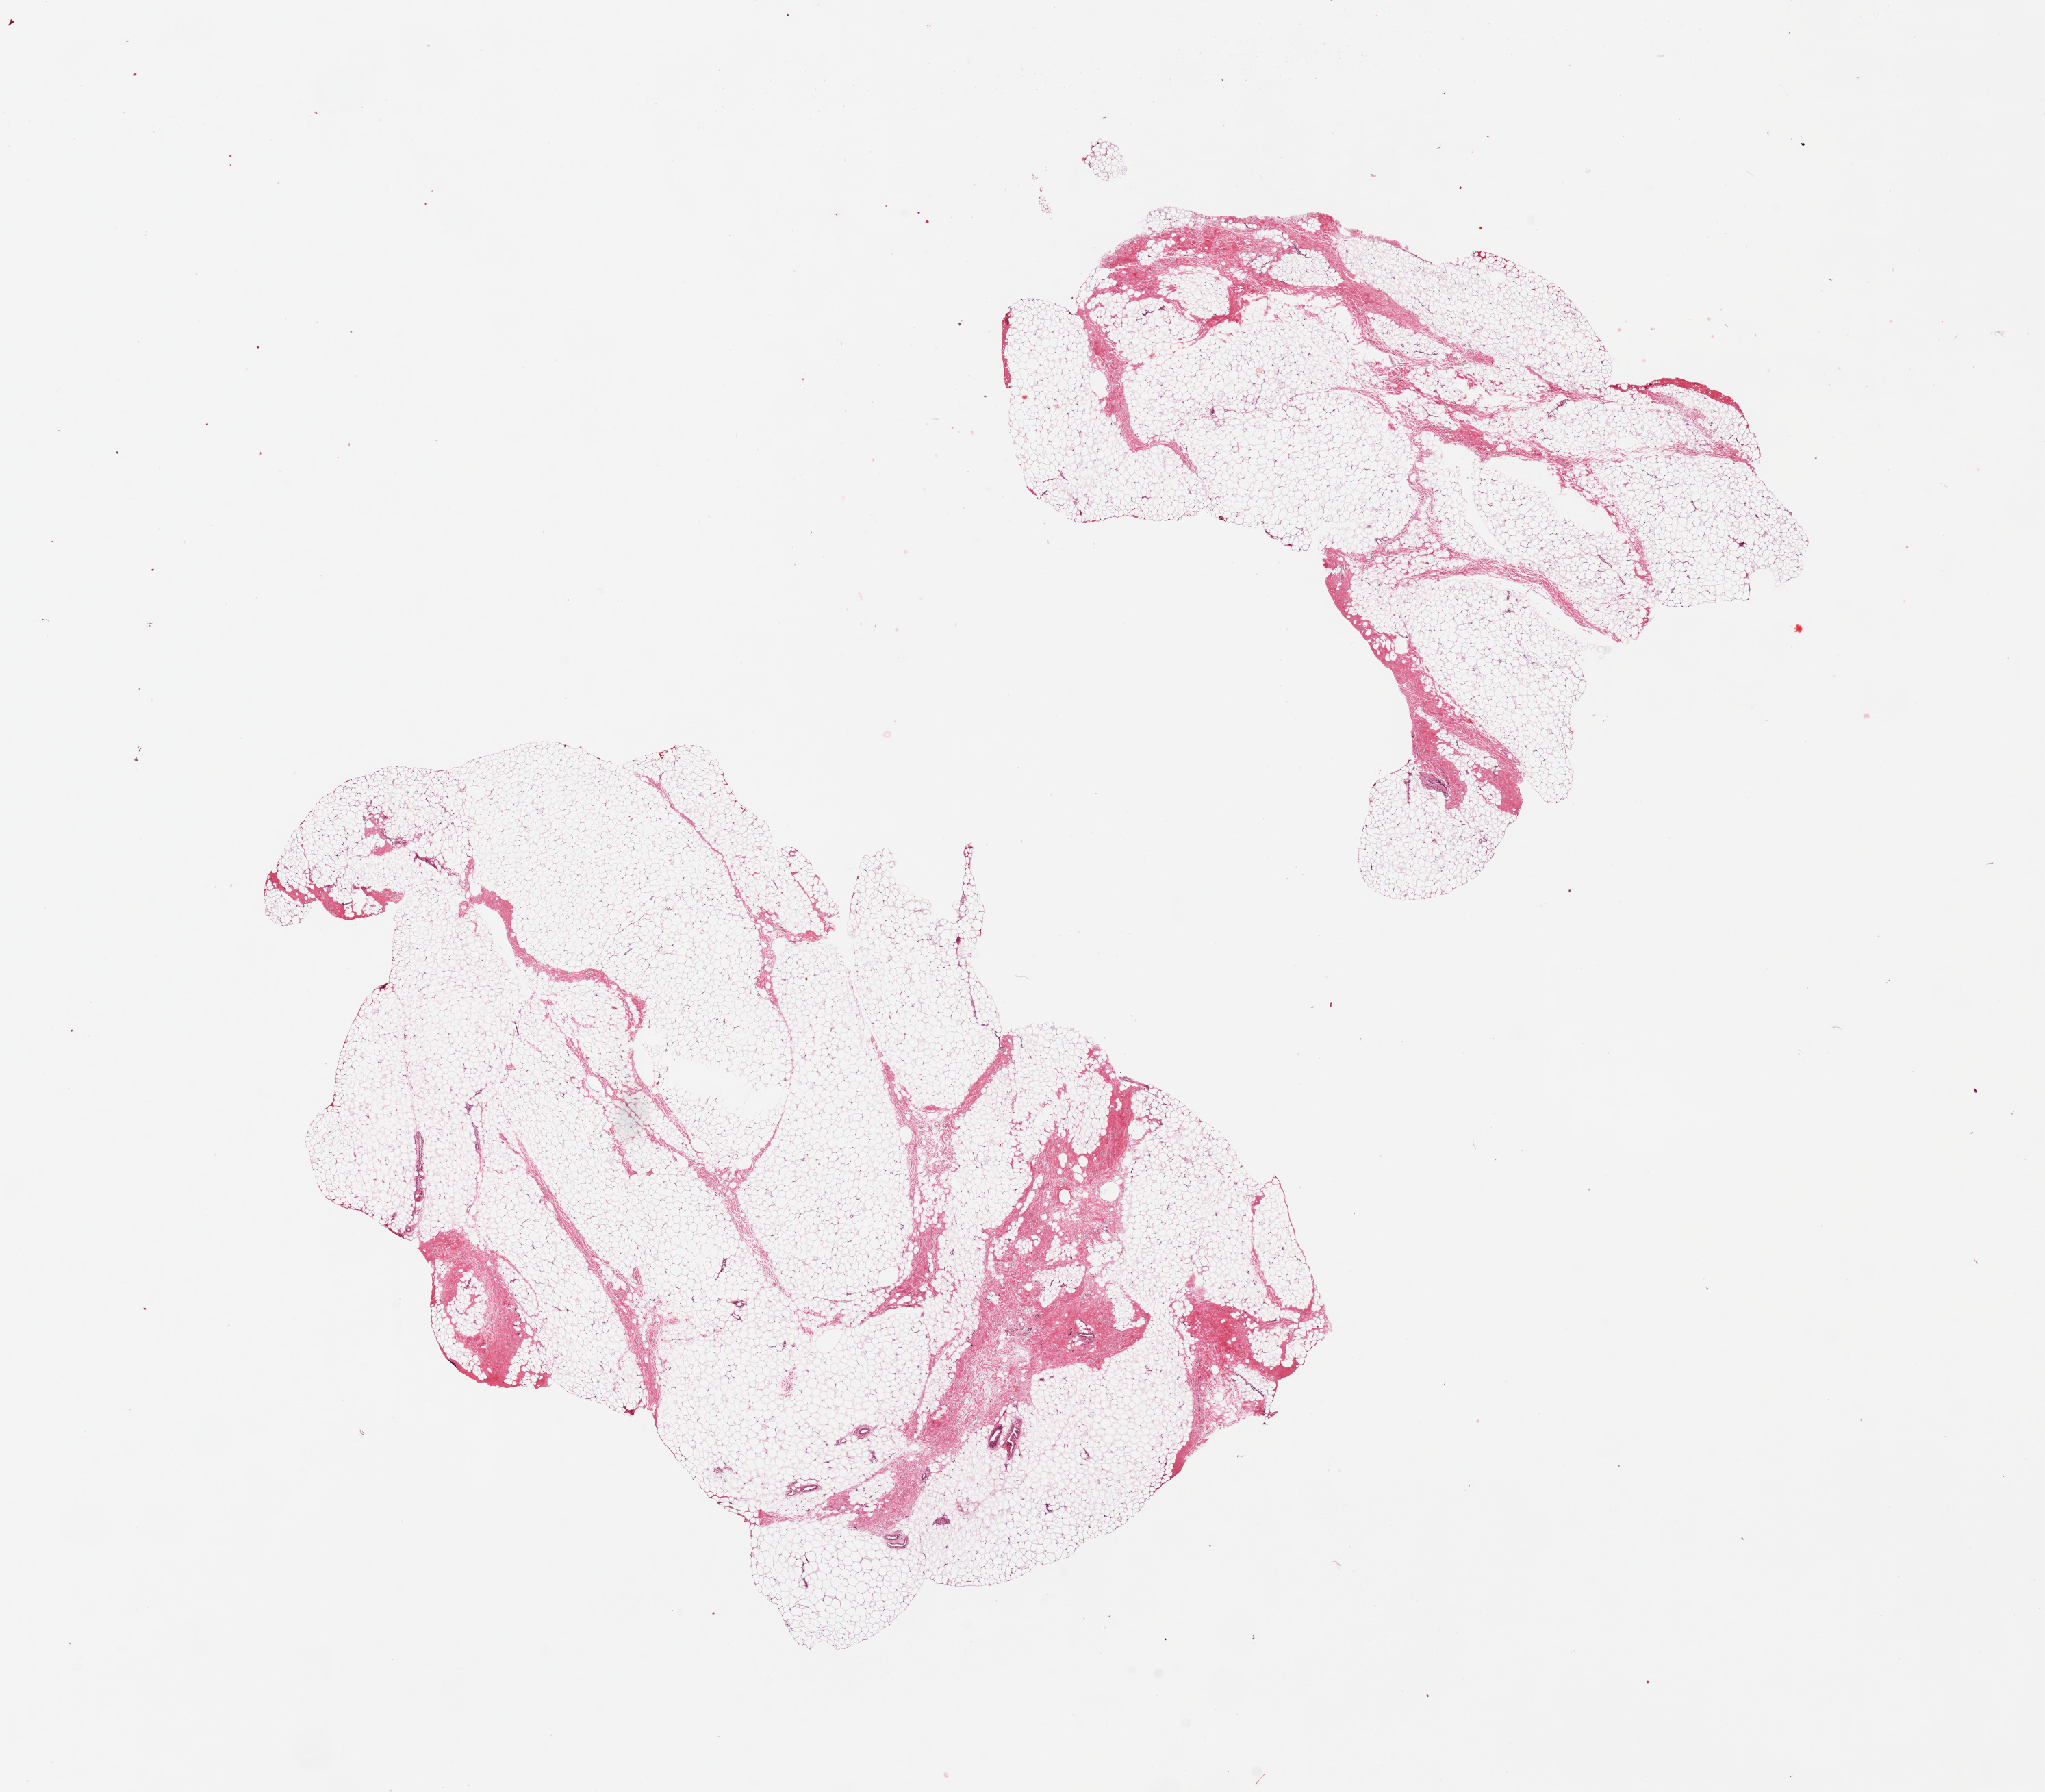
Haematoxylin and eosin whole-slide image, low-resolution overview of the scanned area, about 23.6 x 20.7 mm. PAXgene-fixed paraffin-embedded (PFPE) section. Section of breast (target tissue). Tissue donor sample. Donor sex: male.
Reviewer comment on this tissue sample: 2 pieces; no ductal elements present, all adipose/fibrous tissue (~80%/20%).